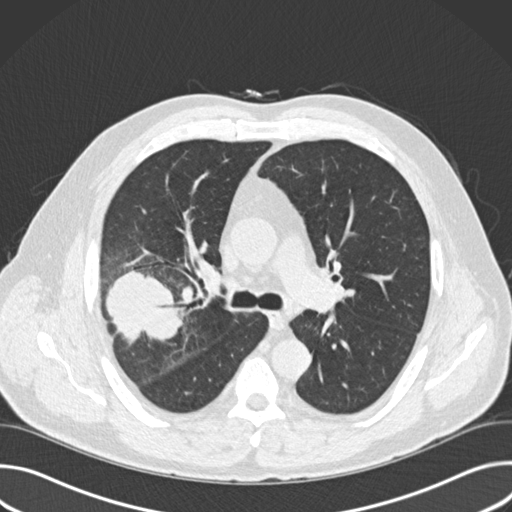
Low-dose screening chest CT, one axial slice; position 103 of 157 along the scan axis; lung window (W 1500 / L -600 HU); 2 mm slice thickness; 512 × 512 image matrix, field of view 380 × 380 mm.
Outlined on this slice (expert manual segmentation):
- lesion 1 (tumor, upper lobe of right lung): box from (x=105, y=270) to (x=188, y=344) px